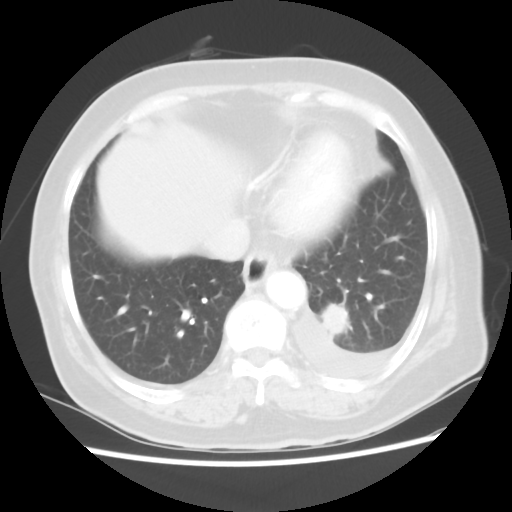
Chest CT, one axial slice; slice 13 of 80 in the series (ordered by position); reconstruction kernel STANDARD; 100 kVp; lung window (W 1500 / L -600 HU); 5 mm slice thickness; 512 × 512 image matrix, field of view 343 × 343 mm. Female patient, age 68 years. From the clinical record (not read from this slice): clinical TNM (as recorded): T1c N0 M1.
Annotated regions visible in this slice (rectangle marked by the reading radiologist):
- lung tumour (recorded histology: adenocarcinoma): bounding box <320,296,354,339> (left, top, right, bottom; pixels)